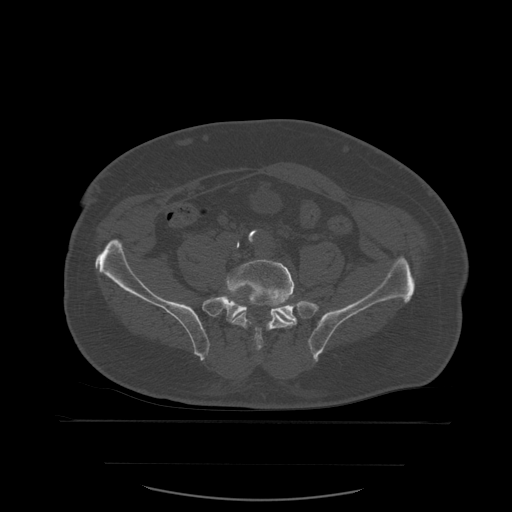
CT including the spine, one axial slice; position 129 of 590 along the scan axis; bone window (W 1800 / L 400 HU); 512 × 512 image matrix. Patient age 71 years. From the clinical record (not read from this slice): primary cancer: lung.
Structures marked on this image (semi-automatically segmented with operator editing):
- L5 vertebra: box from (x=225, y=260) to (x=296, y=351) px